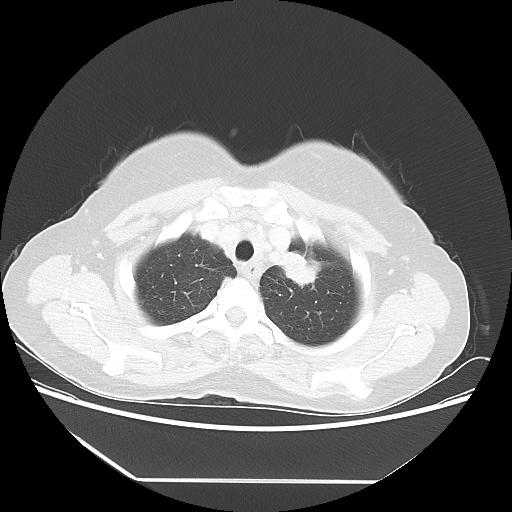
Chest CT, one axial slice; position 45 of 52 along the scan axis; lung window (W 1500 / L -600 HU); 512 × 512 image matrix, field of view 390 × 390 mm. Female patient, age 50 years. Case-level facts recorded for this patient, not image findings: clinical TNM (as recorded): T2 N3 M0.
Annotated regions visible in this slice (bounding box drawn by a radiologist):
- lung tumour (recorded histology: adenocarcinoma): bounding box [x1, y1, x2, y2] px = [273, 240, 332, 296]